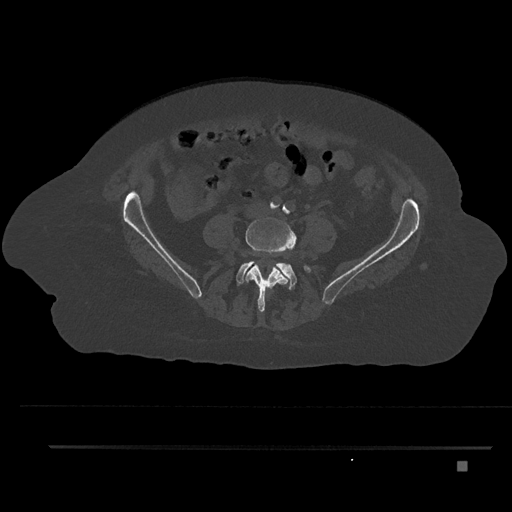
CT including the spine, one axial slice. Position 64 of 797 along the scan axis. 120 kVp. Bone window (W 1800 / L 400 HU). 512 × 512 image matrix, field of view 437 × 437 mm. Female patient, age 76 years. From the clinical record (not read from this slice): primary cancer: lung; vertebrae with lytic lesions (as recorded): T11, L3.
Outlined on this slice (semi-automatic segmentation, software-assisted and operator-edited):
- L4 vertebra: bounding box (x1, y1, x2, y2) in pixels: (245, 217, 296, 312)
- L5 vertebra: (236, 261, 311, 289)